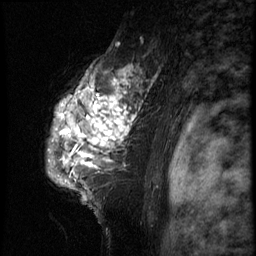
Breast MRI (dynamic contrast-enhanced), one sagittal slice. Slice 53 of 66 in the series (ordered by position). 3 images stored at this slice position (order not interpretable as contrast timing). 1.5 T. TE 4.2 ms, TR 8.9 ms. 2.5 mm slice thickness. 256 × 256 image matrix, field of view 200 × 200 mm. Patient: female, 39 years. From the clinical record (not read from this slice): setting: breast cancer imaged before/during neoadjuvant chemotherapy; receptor status: HER2-positive.
Outlined on this slice (semi-automatic segmentation, software-assisted and operator-edited):
- analysis volume of interest (the breast-tissue region the enhancement analysis was run in; not a lesion): bounding box (x1, y1, x2, y2) in pixels: (42, 44, 166, 196)
- tumour enhancement mask (voxels above the 140 % enhancement threshold inside the analysis volume of interest): (60, 65, 150, 167)